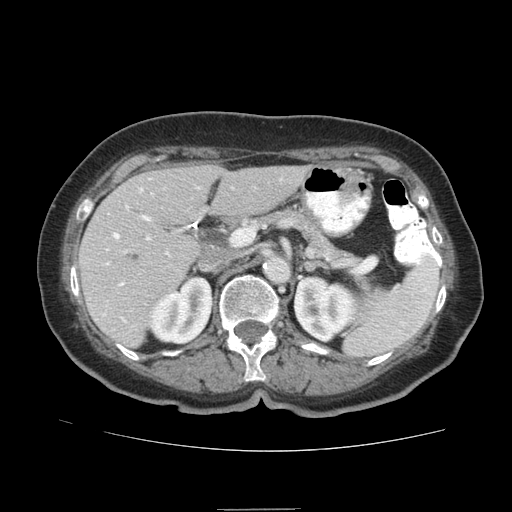
Contrast-enhanced abdominal CT (liver protocol), one axial slice. Slice 42 of 95 in the series (ordered by position). Soft-tissue window (W 400 / L 40 HU). 512 × 512 image matrix. Case-level facts recorded for this patient, not image findings: diagnosis: hepatocellular carcinoma (patient treated with transarterial chemoembolisation; whether this scan precedes or follows treatment is not stated here); TNM stage (as recorded): Stage-IVA; Child-Pugh class: B; tumour nodularity: uninodular.
Outlined on this slice (semi-automatic segmentation, software-assisted and operator-edited):
- liver parenchyma outside the tumour (the mass and vessels are separate outlines, so this box may not span the whole liver): bounding box (x1, y1, x2, y2) in pixels: (78, 164, 310, 346)
- liver vessels: (104, 188, 191, 322)